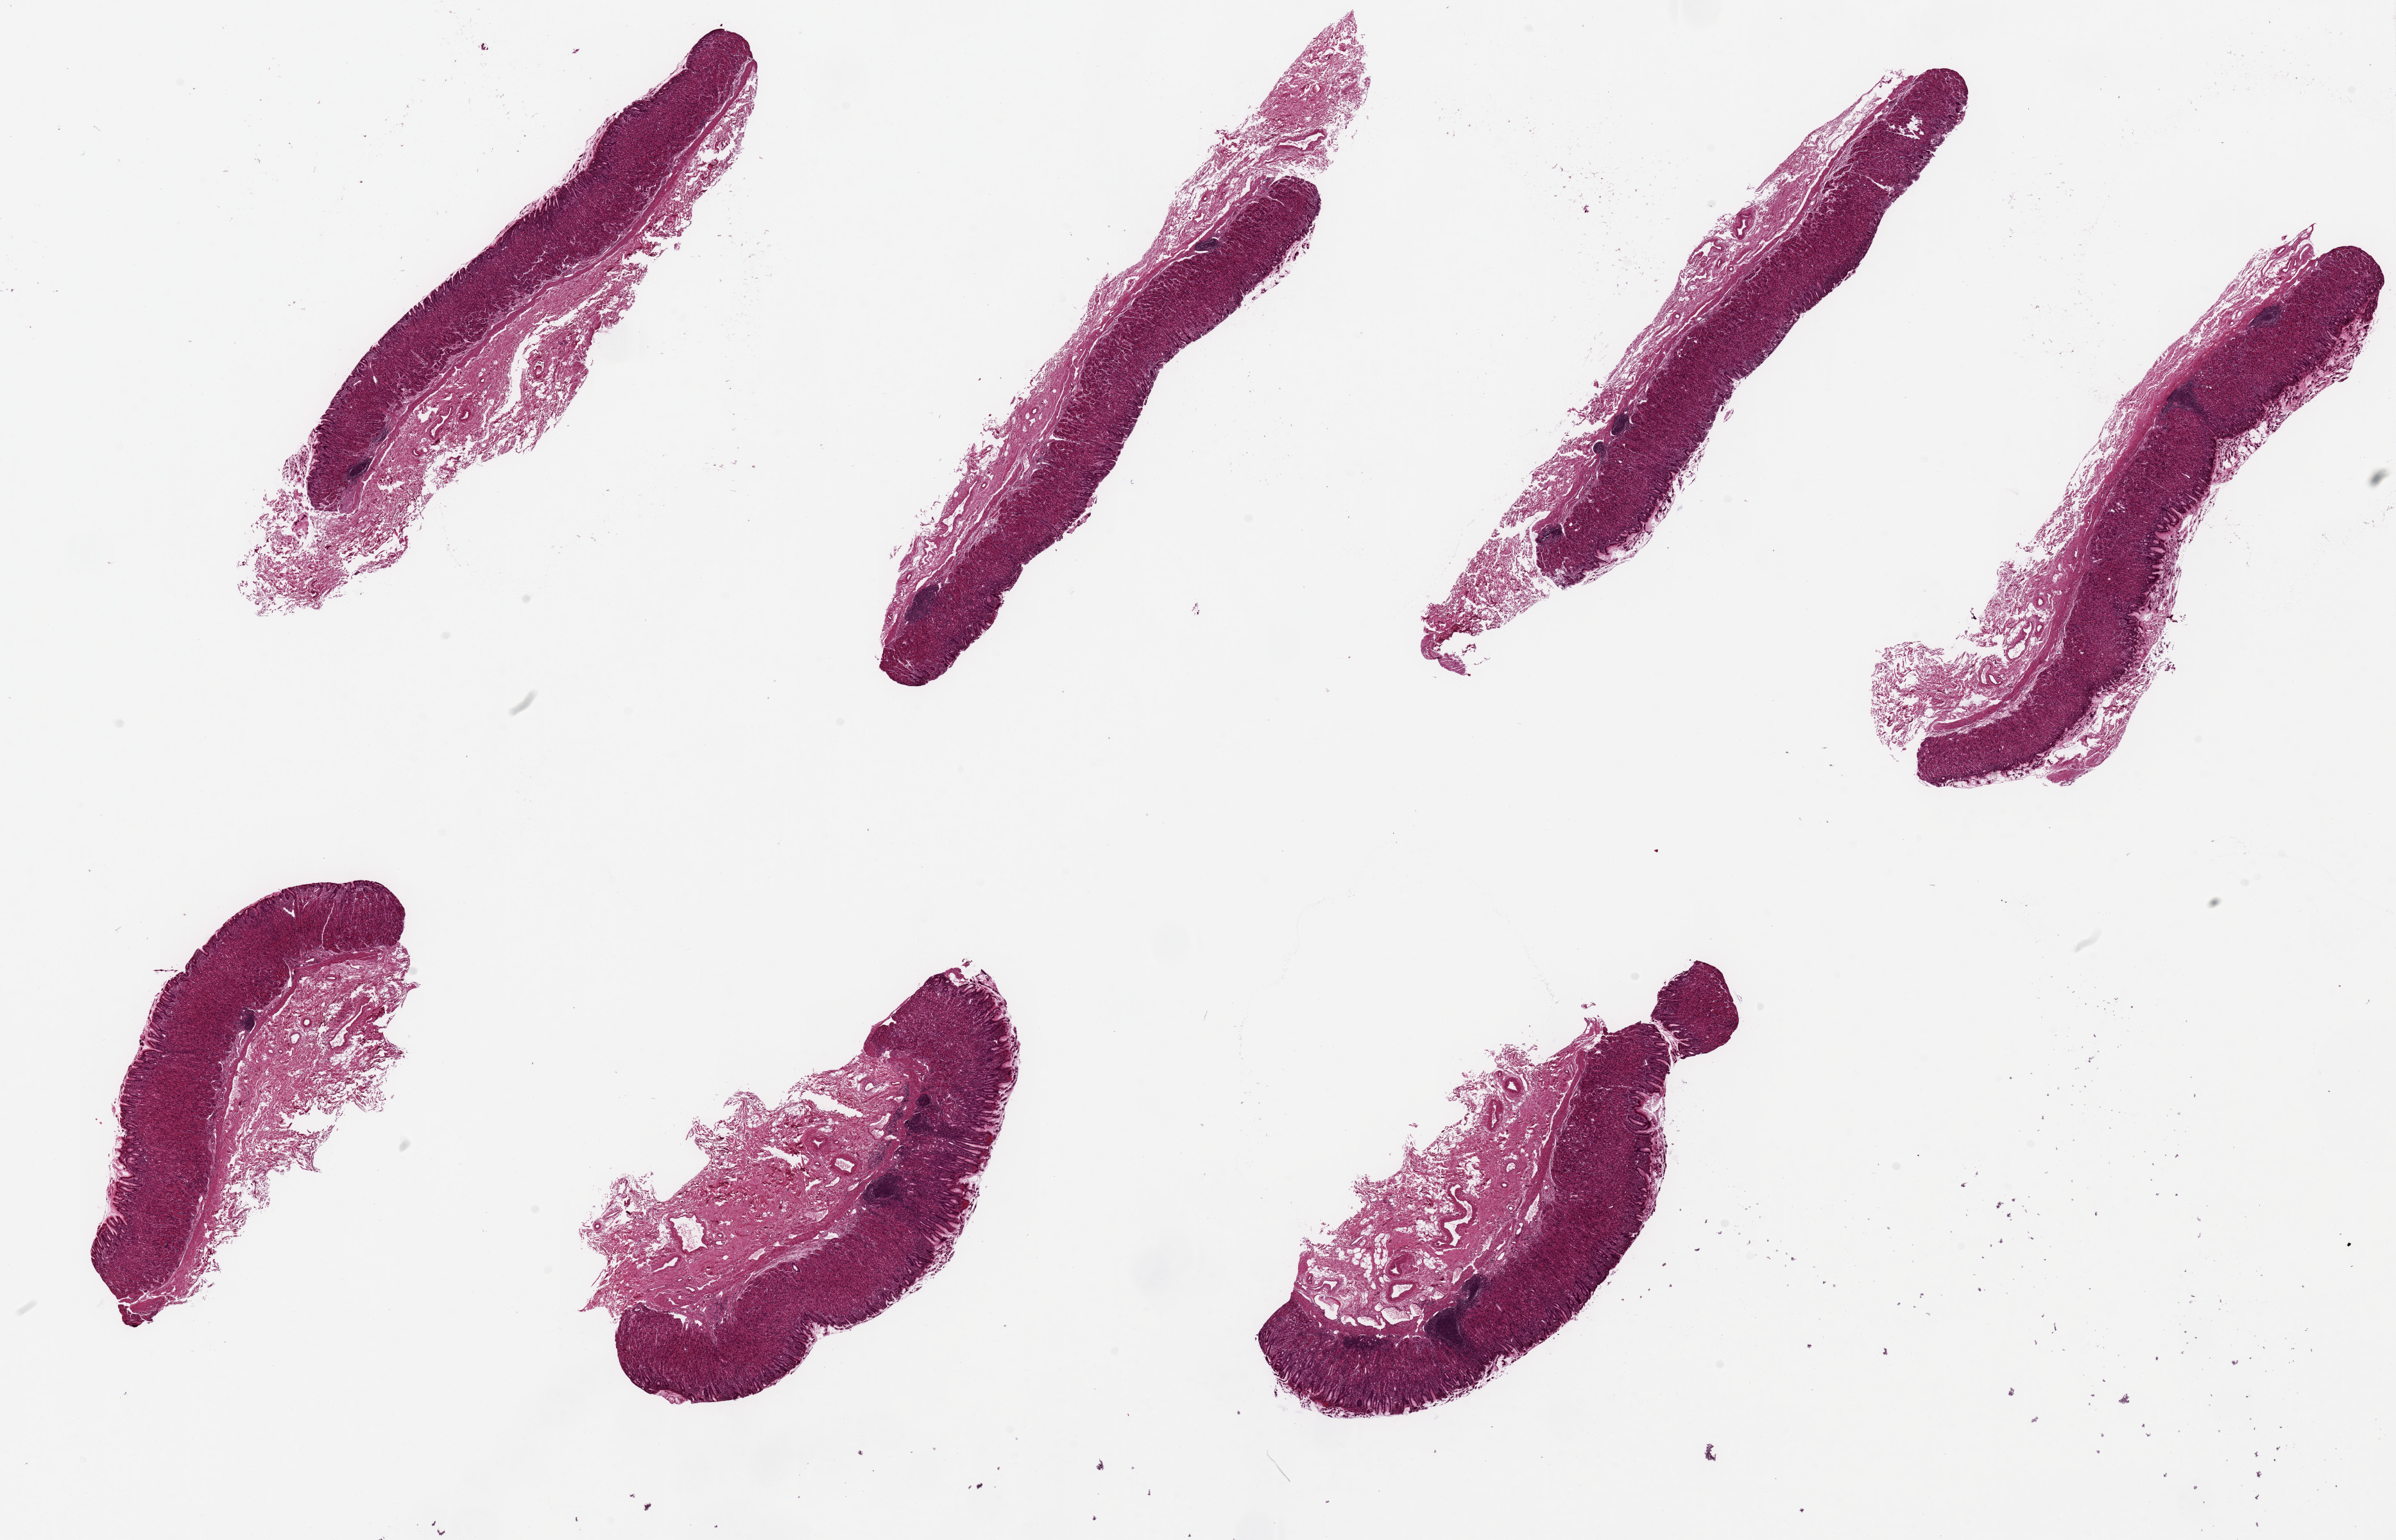
H&E whole-slide image — low-resolution overview of the scanned area, about 29.5 x 19.0 mm; PAXgene-fixed, paraffin-embedded tissue; sampled site (target tissue): stomach; tissue donor sample. Donor sex: male.
Pathologist's review note for this sample: 7 pieces up to 9x3 mm; chronic gastritis; oxyntic mucosa.